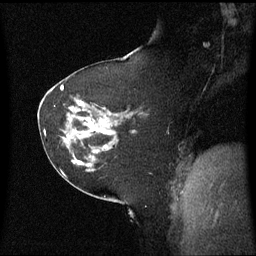
Breast MRI (dynamic contrast-enhanced), one sagittal slice; slice 33 of 60 in the series (ordered by position); dynamic contrast-enhanced series, image 2 of 3 at this slice position (ordered by acquisition); 1.5 T; TE 4.2 ms, TR 8.4 ms; 2.2 mm slice thickness; 256 × 256 image matrix, field of view 220 × 220 mm. Patient: female, 60 years. From the clinical record (not read from this slice): setting: breast cancer imaged before/during neoadjuvant chemotherapy; receptor status: triple-negative.
Structures marked on this image (semi-automatically segmented with operator editing):
- analysis volume of interest (the breast-tissue region the enhancement analysis was run in; not a lesion): bounding box <62,98,128,161> (left, top, right, bottom; pixels)
- tumour enhancement mask (voxels above the 70 % enhancement threshold inside the analysis volume of interest): <90,126,106,147>